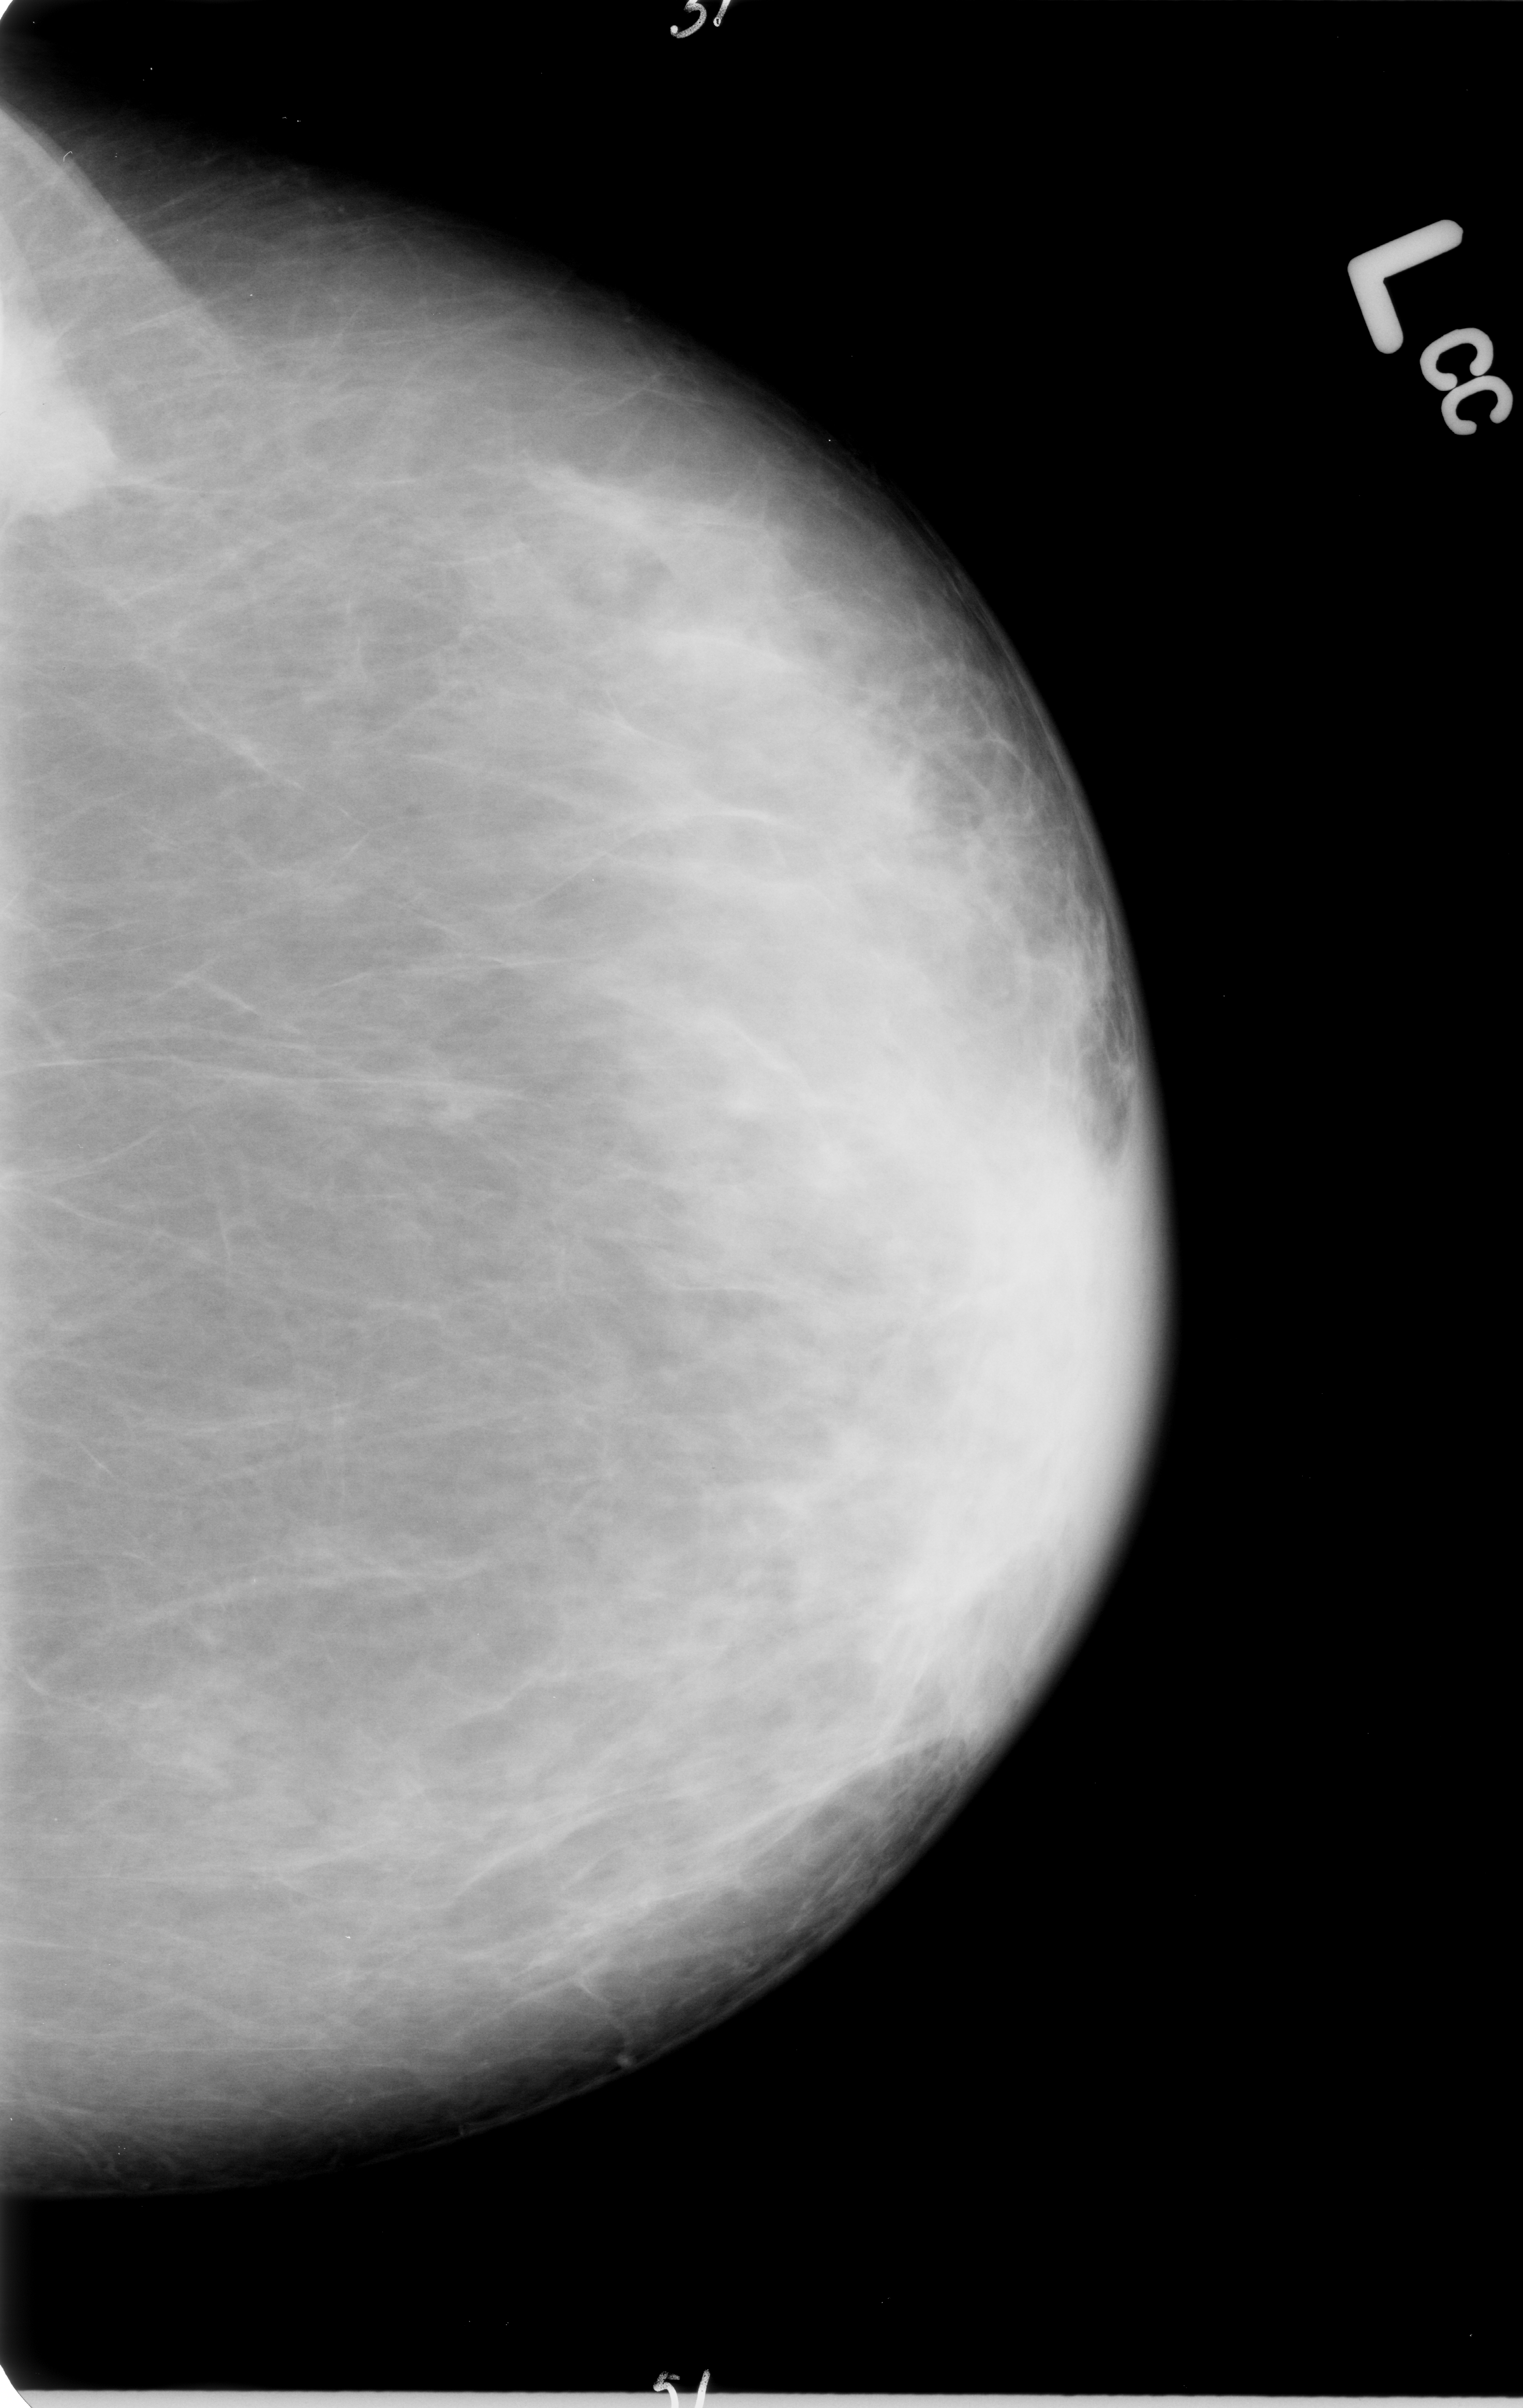
Digitized screen-film mammogram. Left breast. Craniocaudal (CC) view. Breast composition: heterogeneously dense (BI-RADS density category 3 of 4). 1523 × 2408 image matrix.
Marked abnormalities (boxes around the expert regions of interest):
- mass, shape irregular, margins spiculated; BI-RADS assessment category 4; subtlety rating 4 on a 1 (subtle) to 5 (obvious) scale; pathology result (as recorded, not read from the image): malignant: bounding box (x1, y1, x2, y2) in pixels: (0, 360, 147, 561)